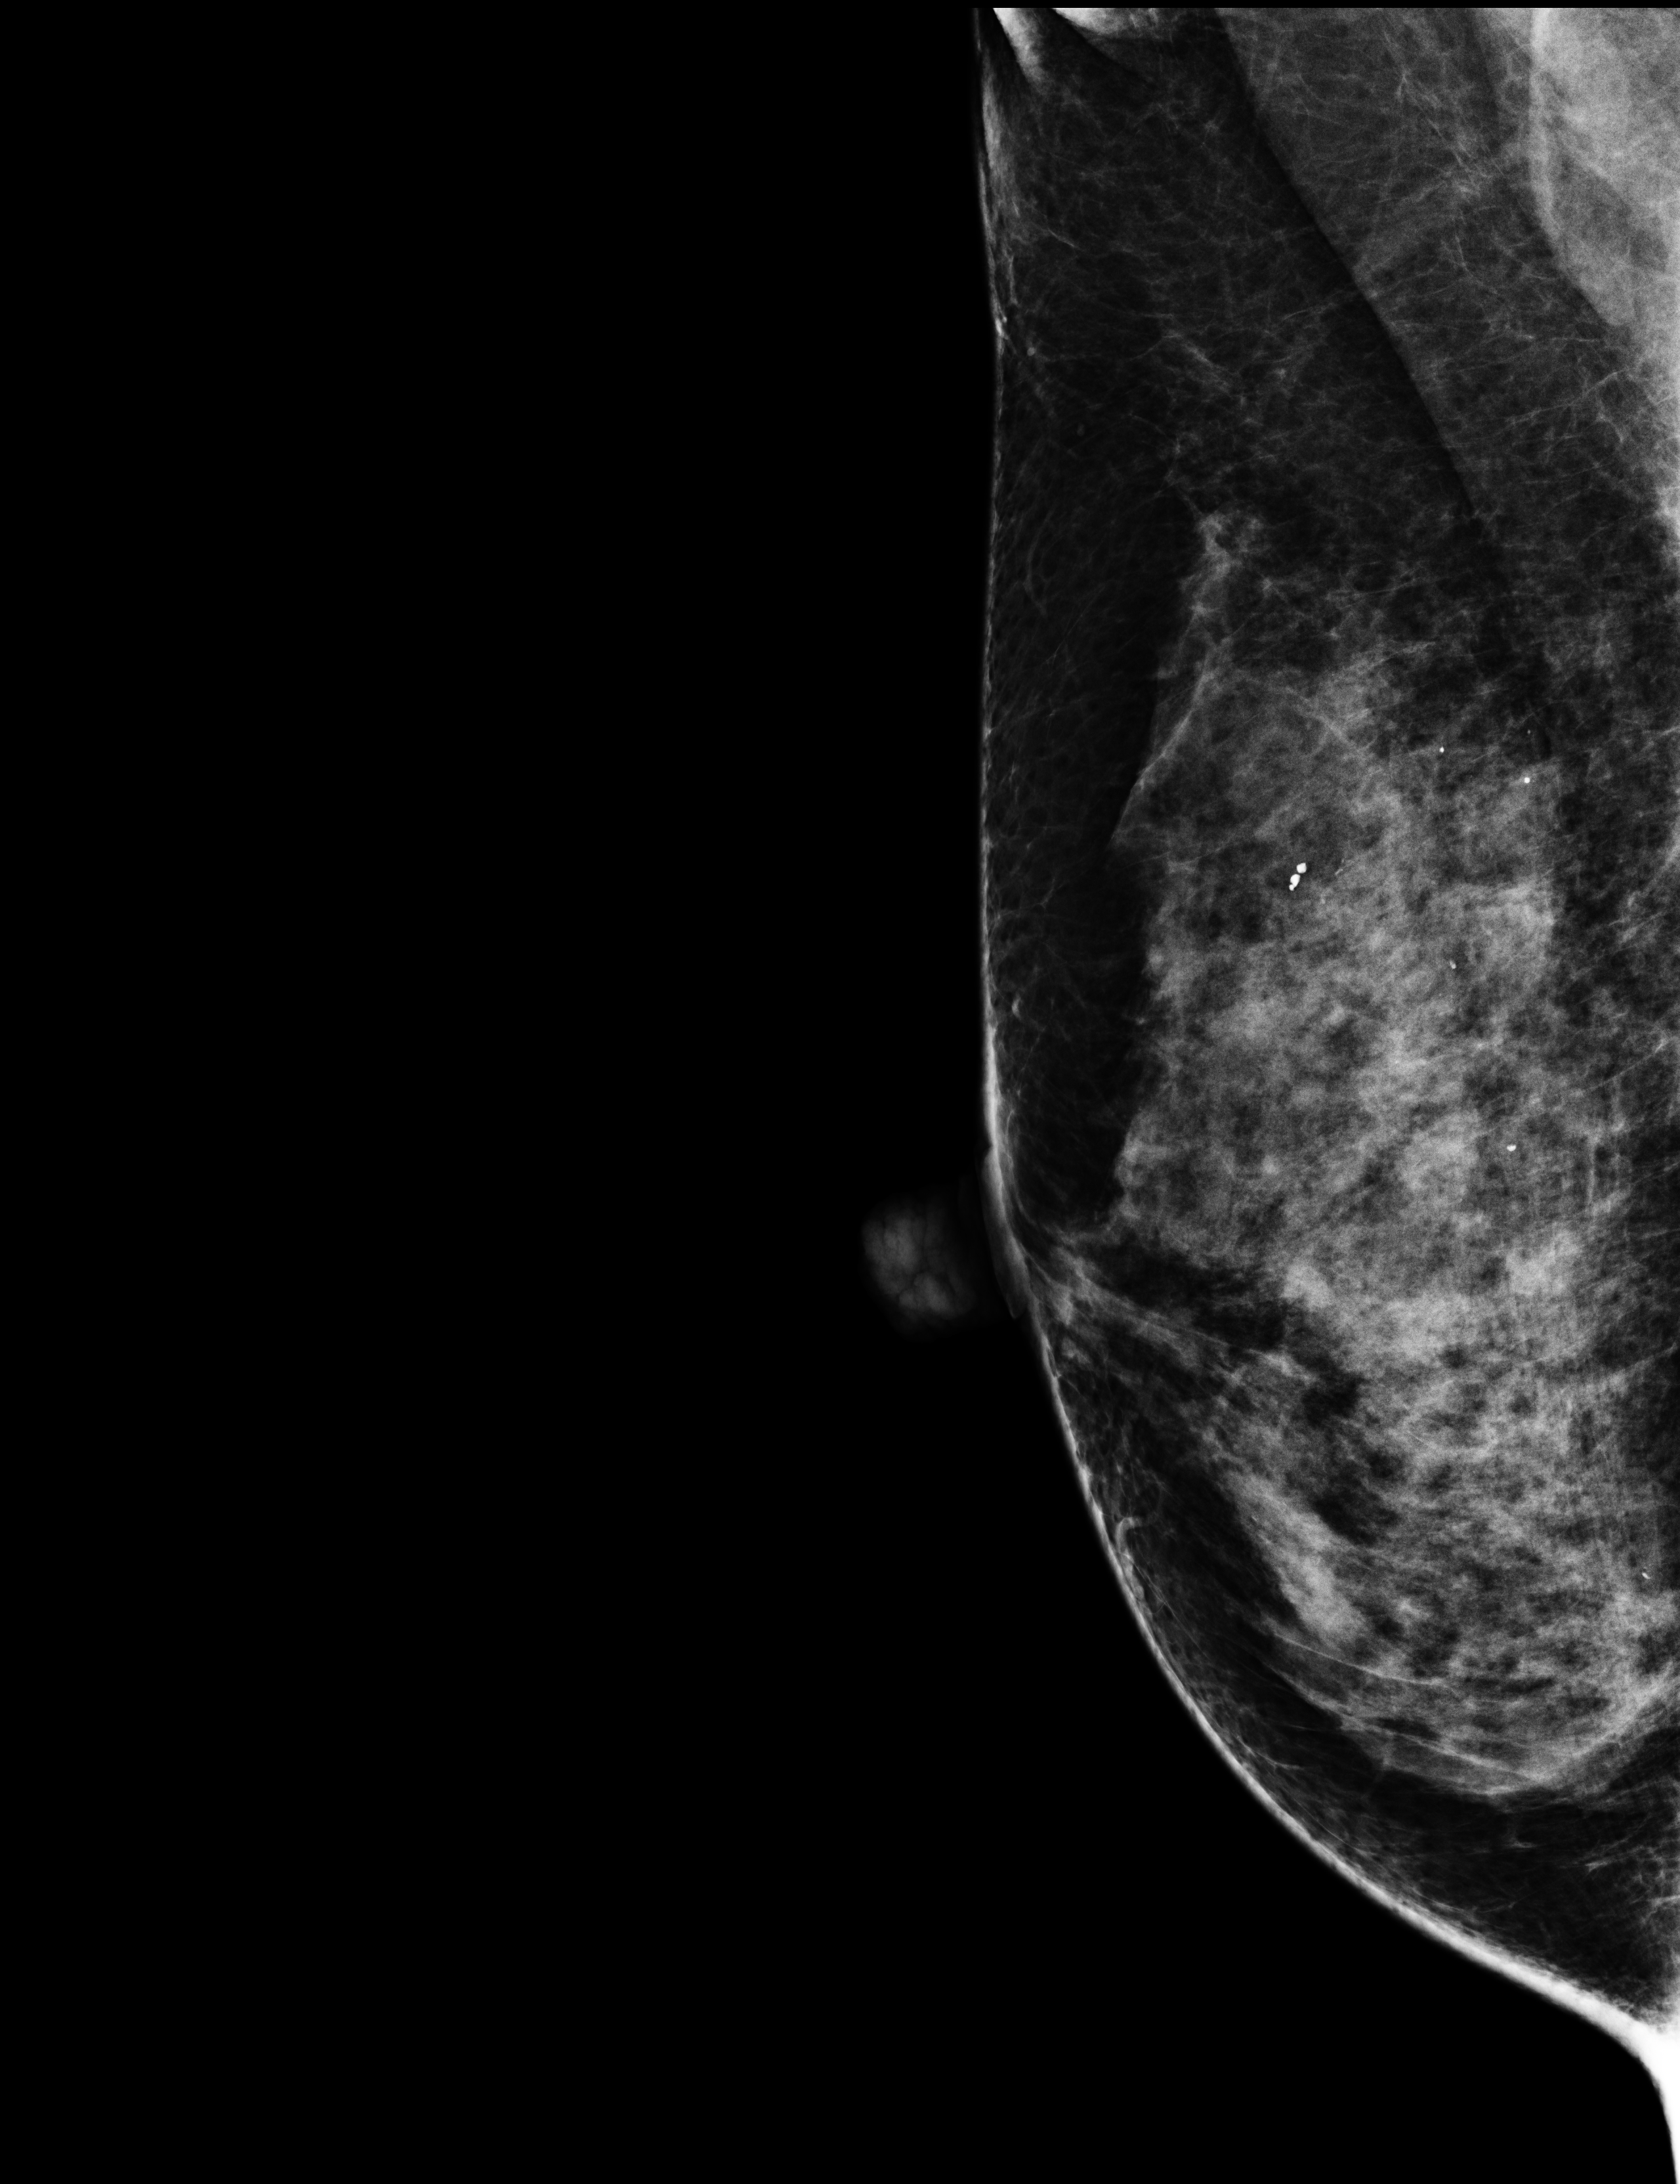
Full-field digital mammogram (FFDM), right breast, mediolateral oblique (MLO) view, screening examination. Patient aged 53 years (female).
- breast density at the screening exam (both breasts): extremely dense (BI-RADS density category d)
- final BI-RADS category for the screening round (tomosynthesis exam, both breasts): category 2
- recall: no recall after this screen